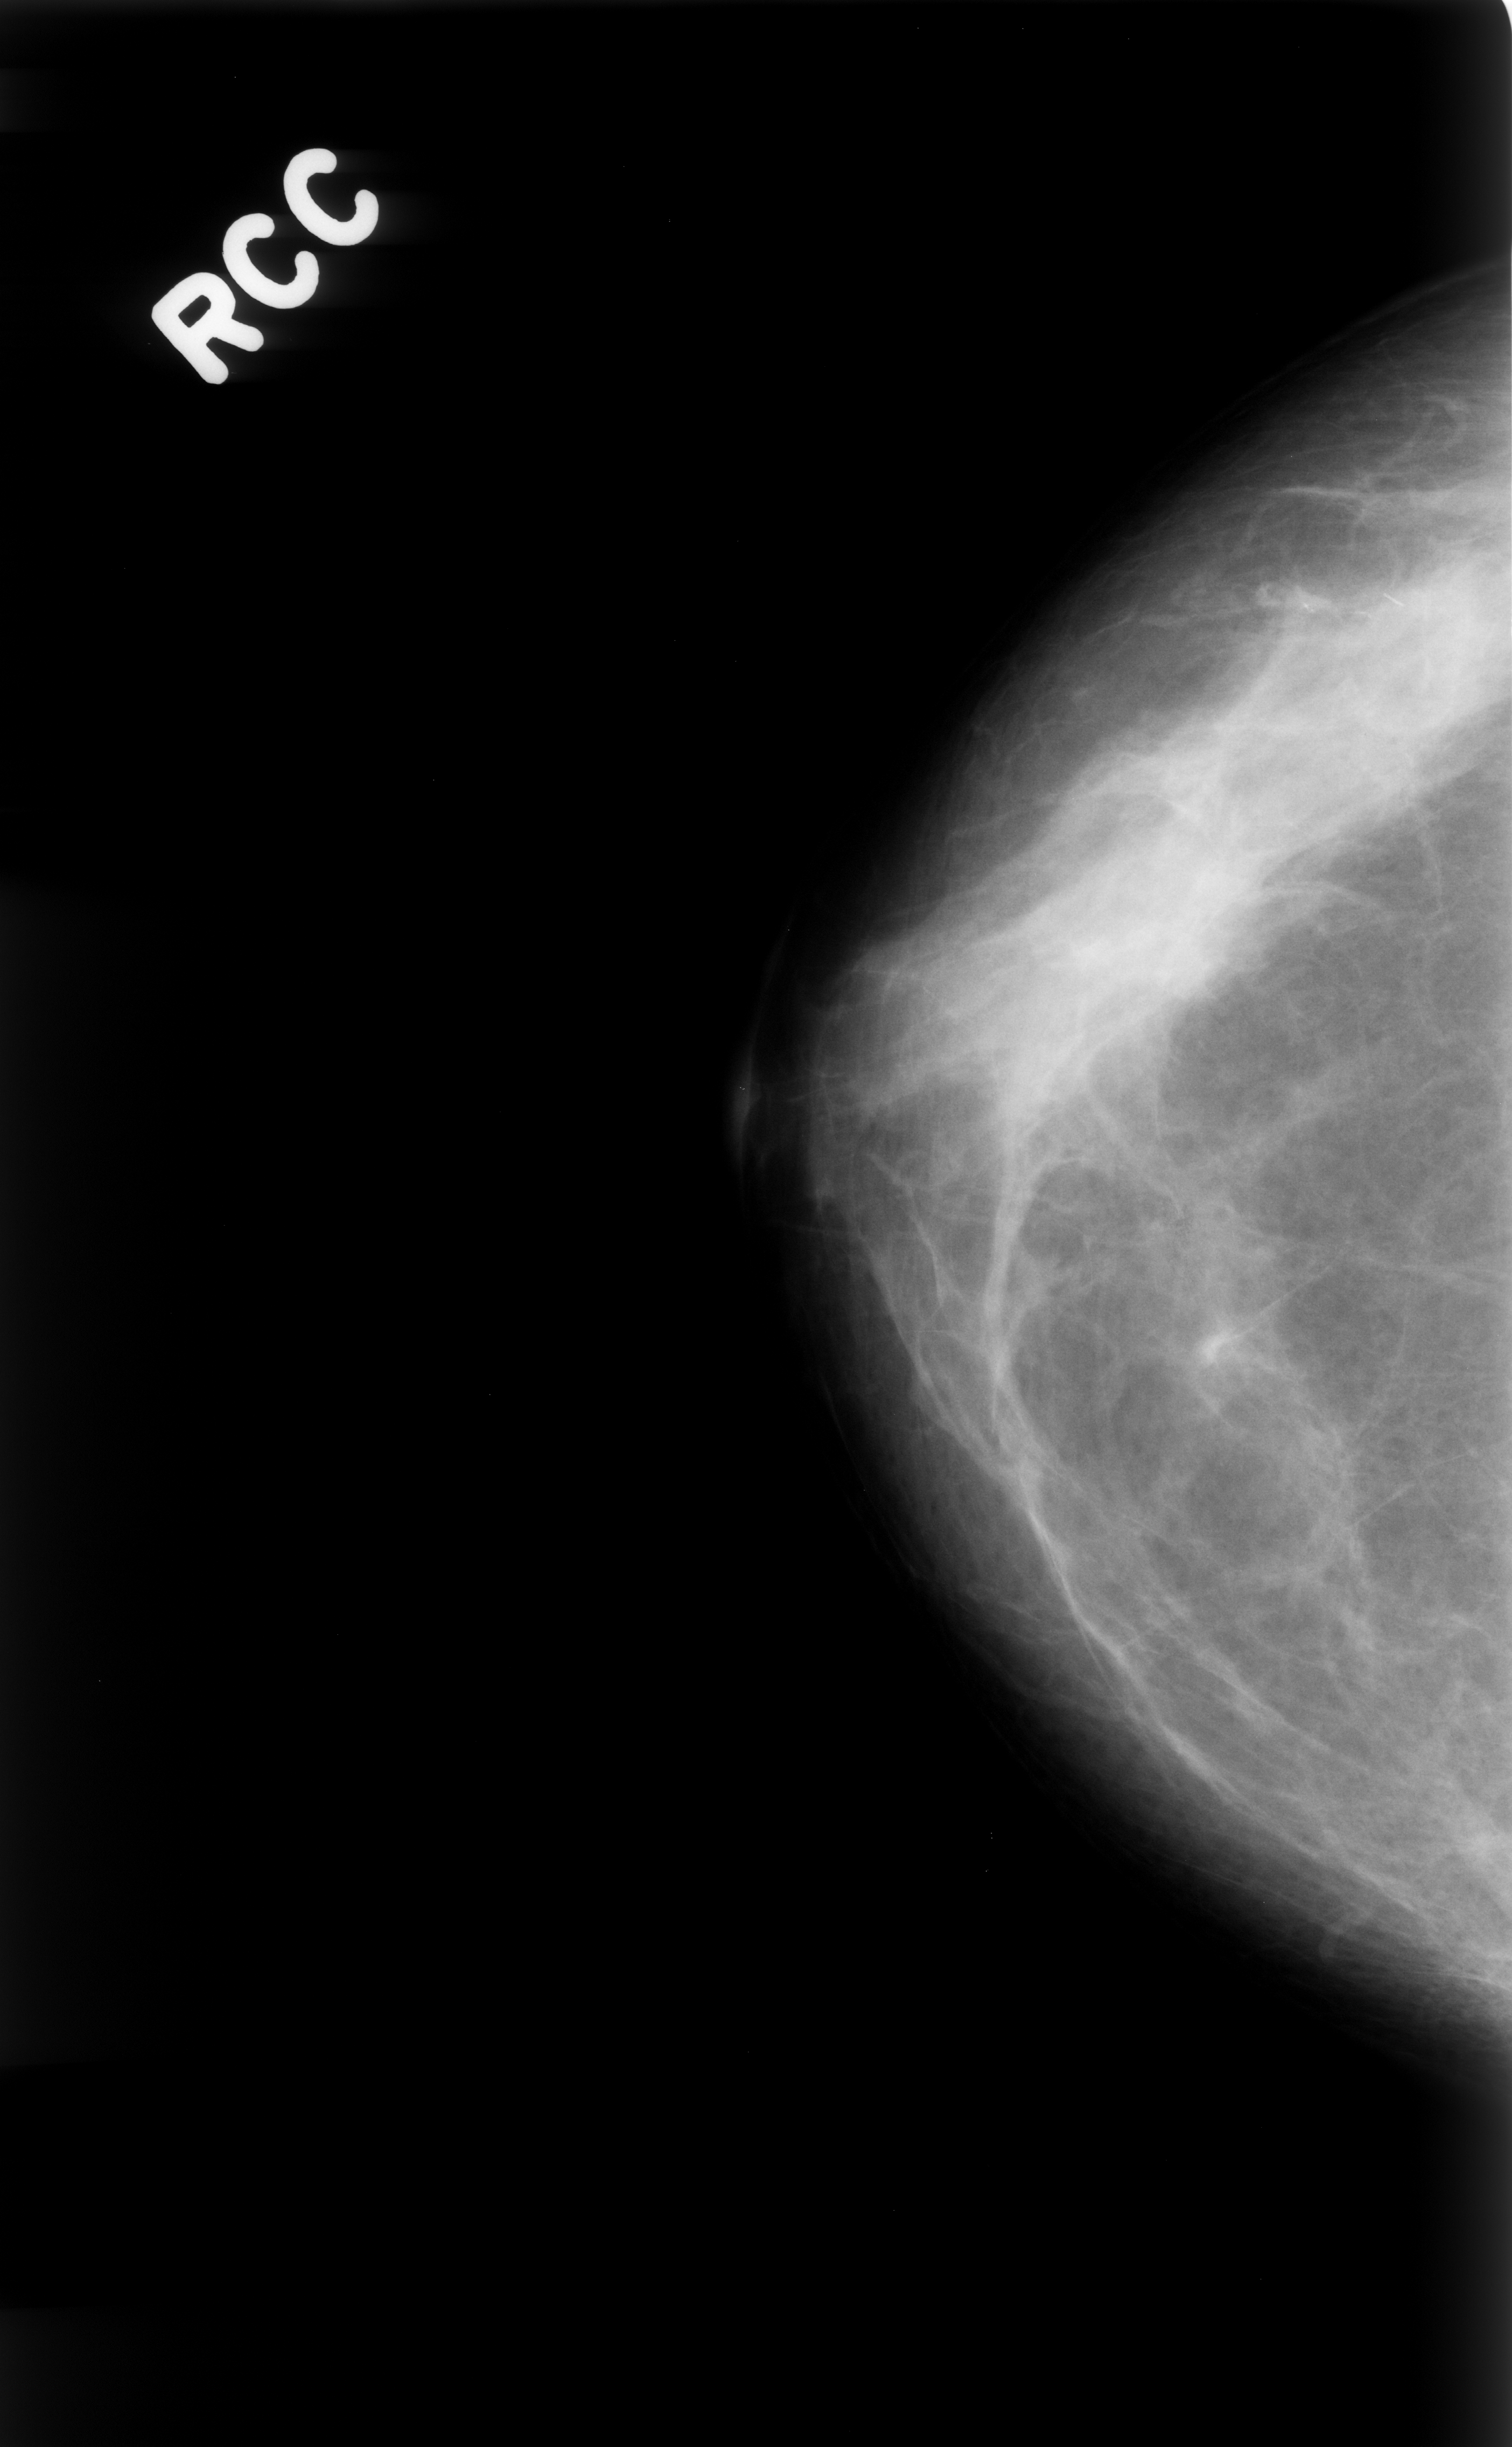
Digitized screen-film mammogram, right breast, CC view, BI-RADS breast density category 2 (scale 1–4).
Abnormality record for this image: calcifications, morphology fine linear branching, distribution linear; BI-RADS assessment category 4; pathology (as recorded): benign.